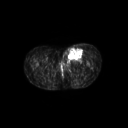
FDG PET of an extremity soft-tissue mass (from a PET/CT study), one axial slice. Position 48 of 267 along the scan axis. 128 × 128 image matrix, field of view 600 × 600 mm. Female patient, age 24 years. From the clinical record (not read from this slice): histological type: leiomyosarcoma; grade: high; site of the primary tumour: groin.
Annotated regions visible in this slice (expert contour drawn on MRI and transferred to this co-registered scan by the dataset authors):
- gross tumour volume including surrounding oedema: box from (x=62, y=46) to (x=83, y=62) px
- gross tumour volume (mass): (x=67, y=48)–(x=83, y=59)